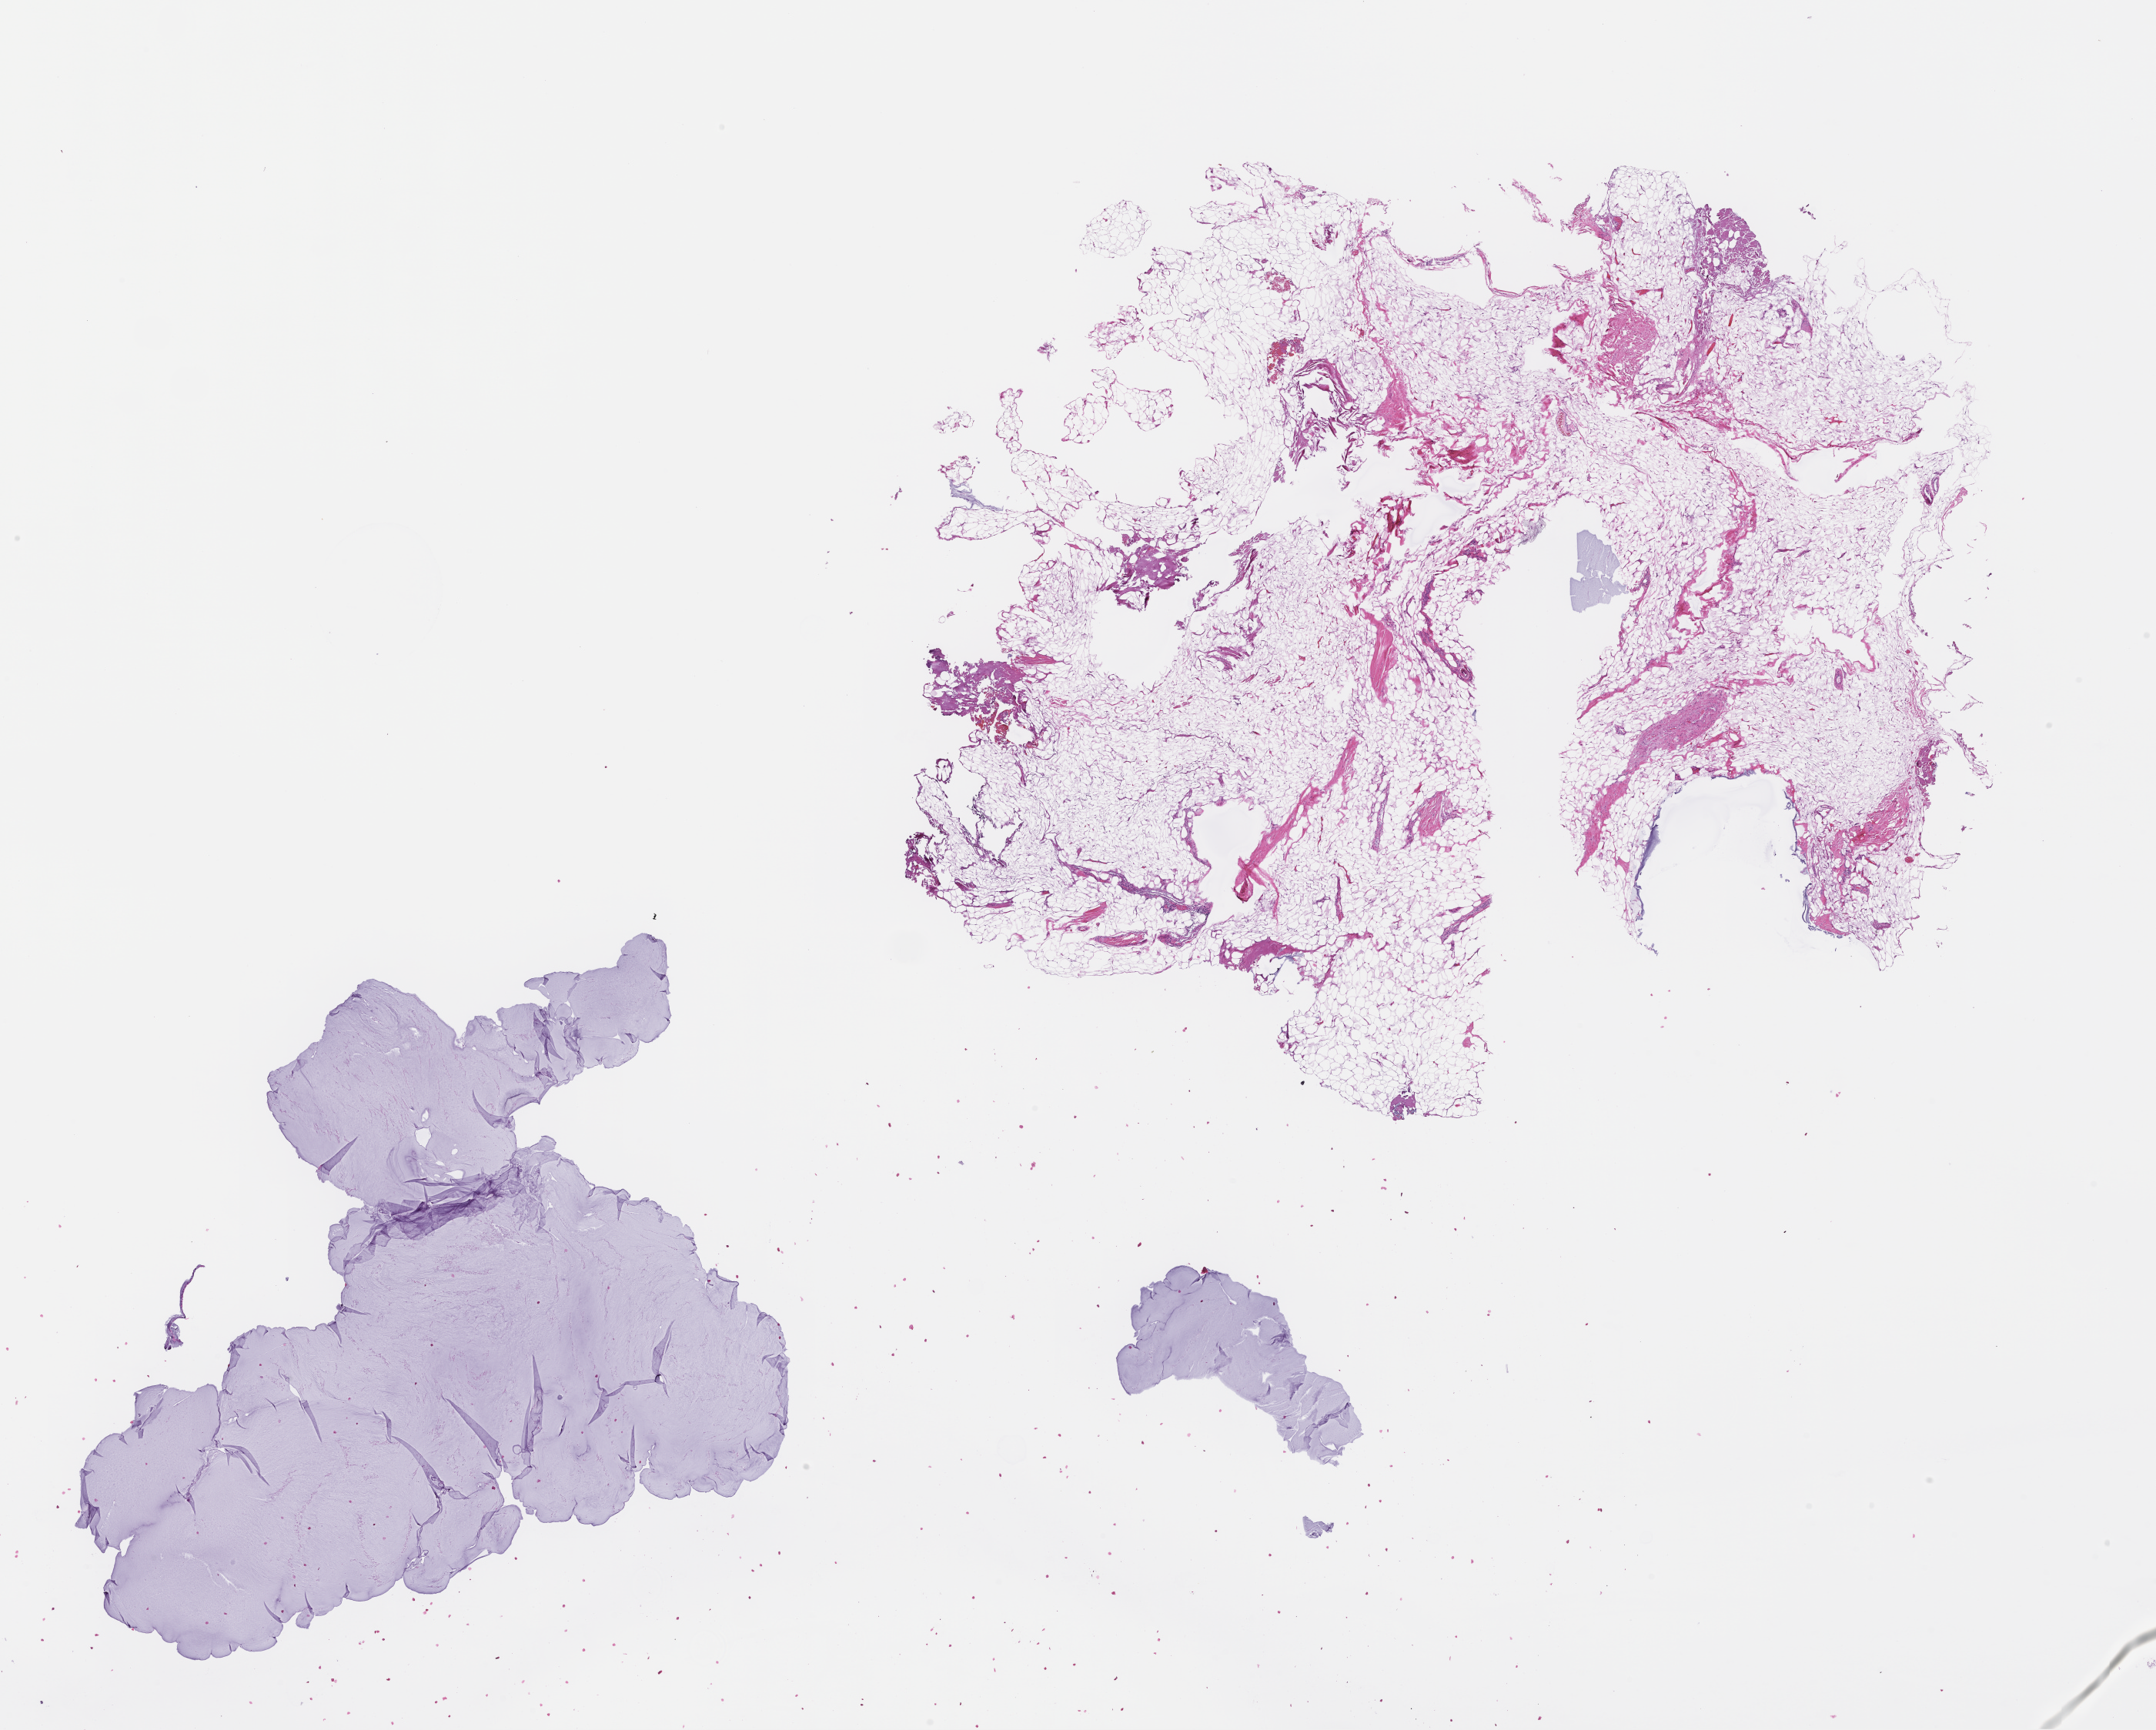
Digitized H&E-stained section — a low-resolution overview of the entire scanned area, about 22.6 x 18.2 mm, formalin-fixed, paraffin-embedded (FFPE) tissue, specimen time point: collected at baseline (before treatment). Patient sex: male.
- this section: metastasis (sampled organ not recorded)
- primary diagnosis of the patient: Colorectal Carcinoma